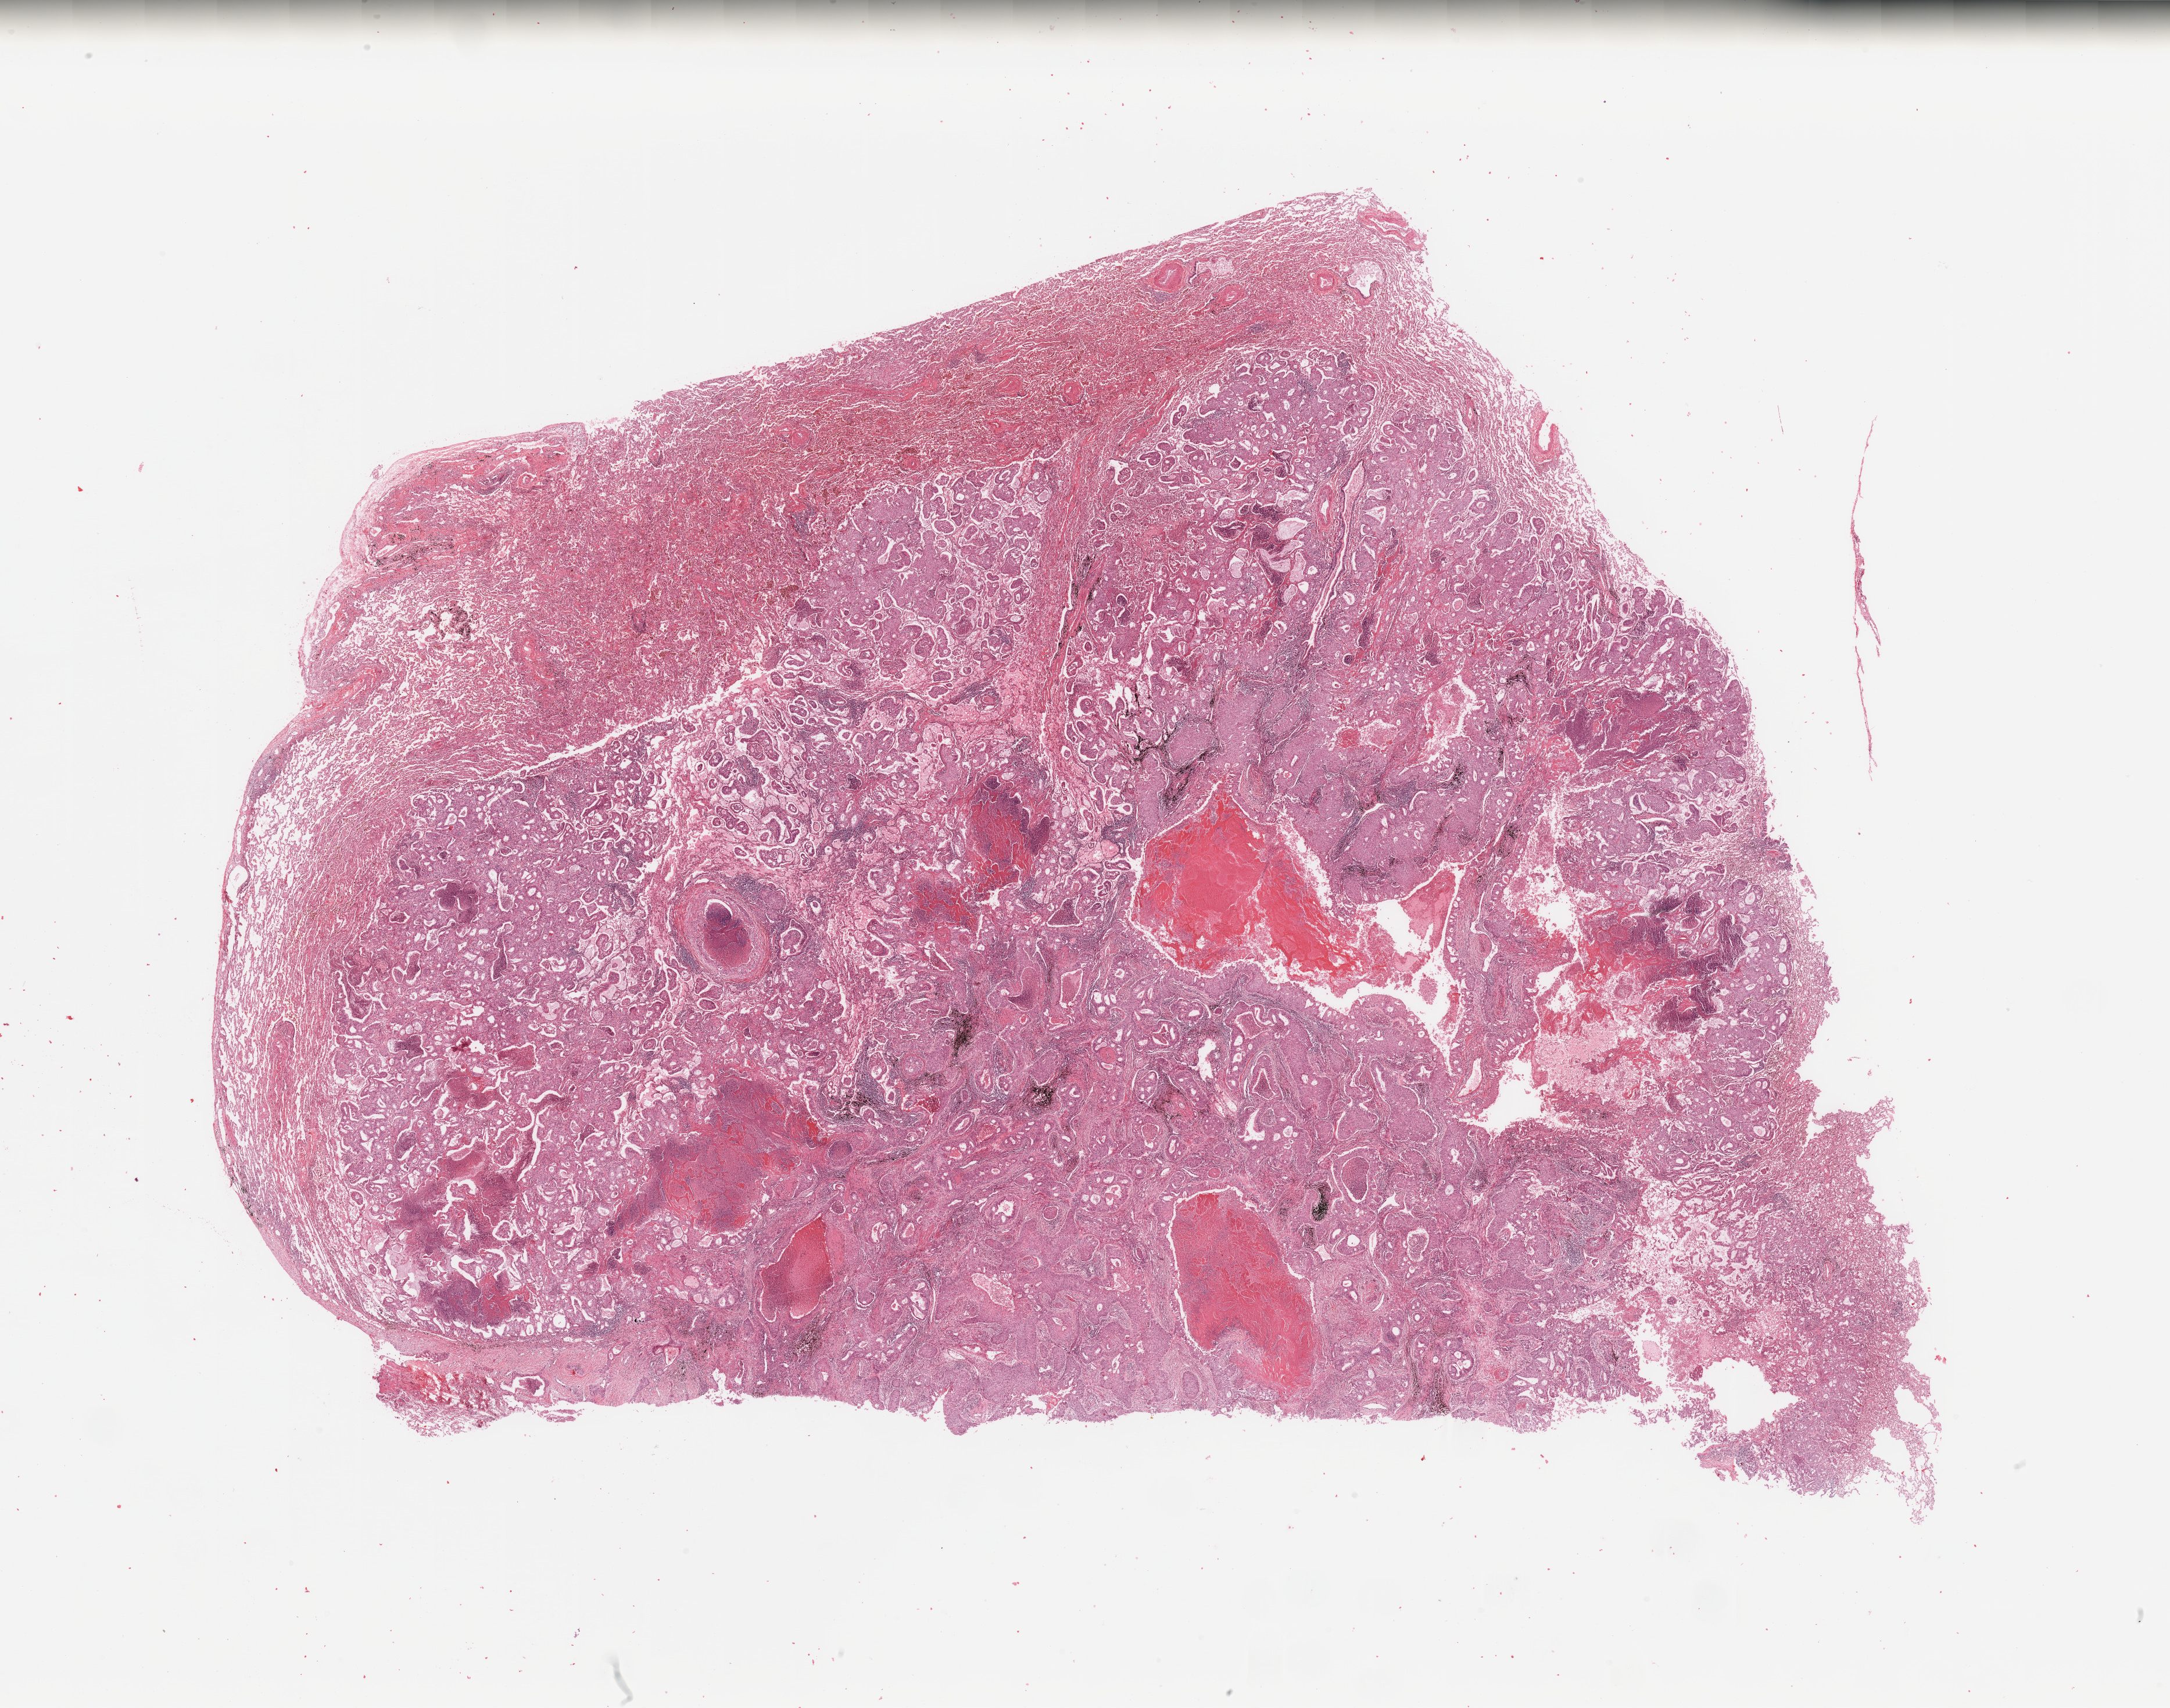
Whole-slide histology image, Hematoxylin and eosin (H&E) stained — low-resolution overview of the scanned area, about 29.5 x 23.2 mm; tumour tissue sample, lung. 61-year-old male patient. Histologic grade: G3 (poorly differentiated).
Histologic diagnosis: Adenocarcinoma, NOS. AJCC pathologic stage: IB.